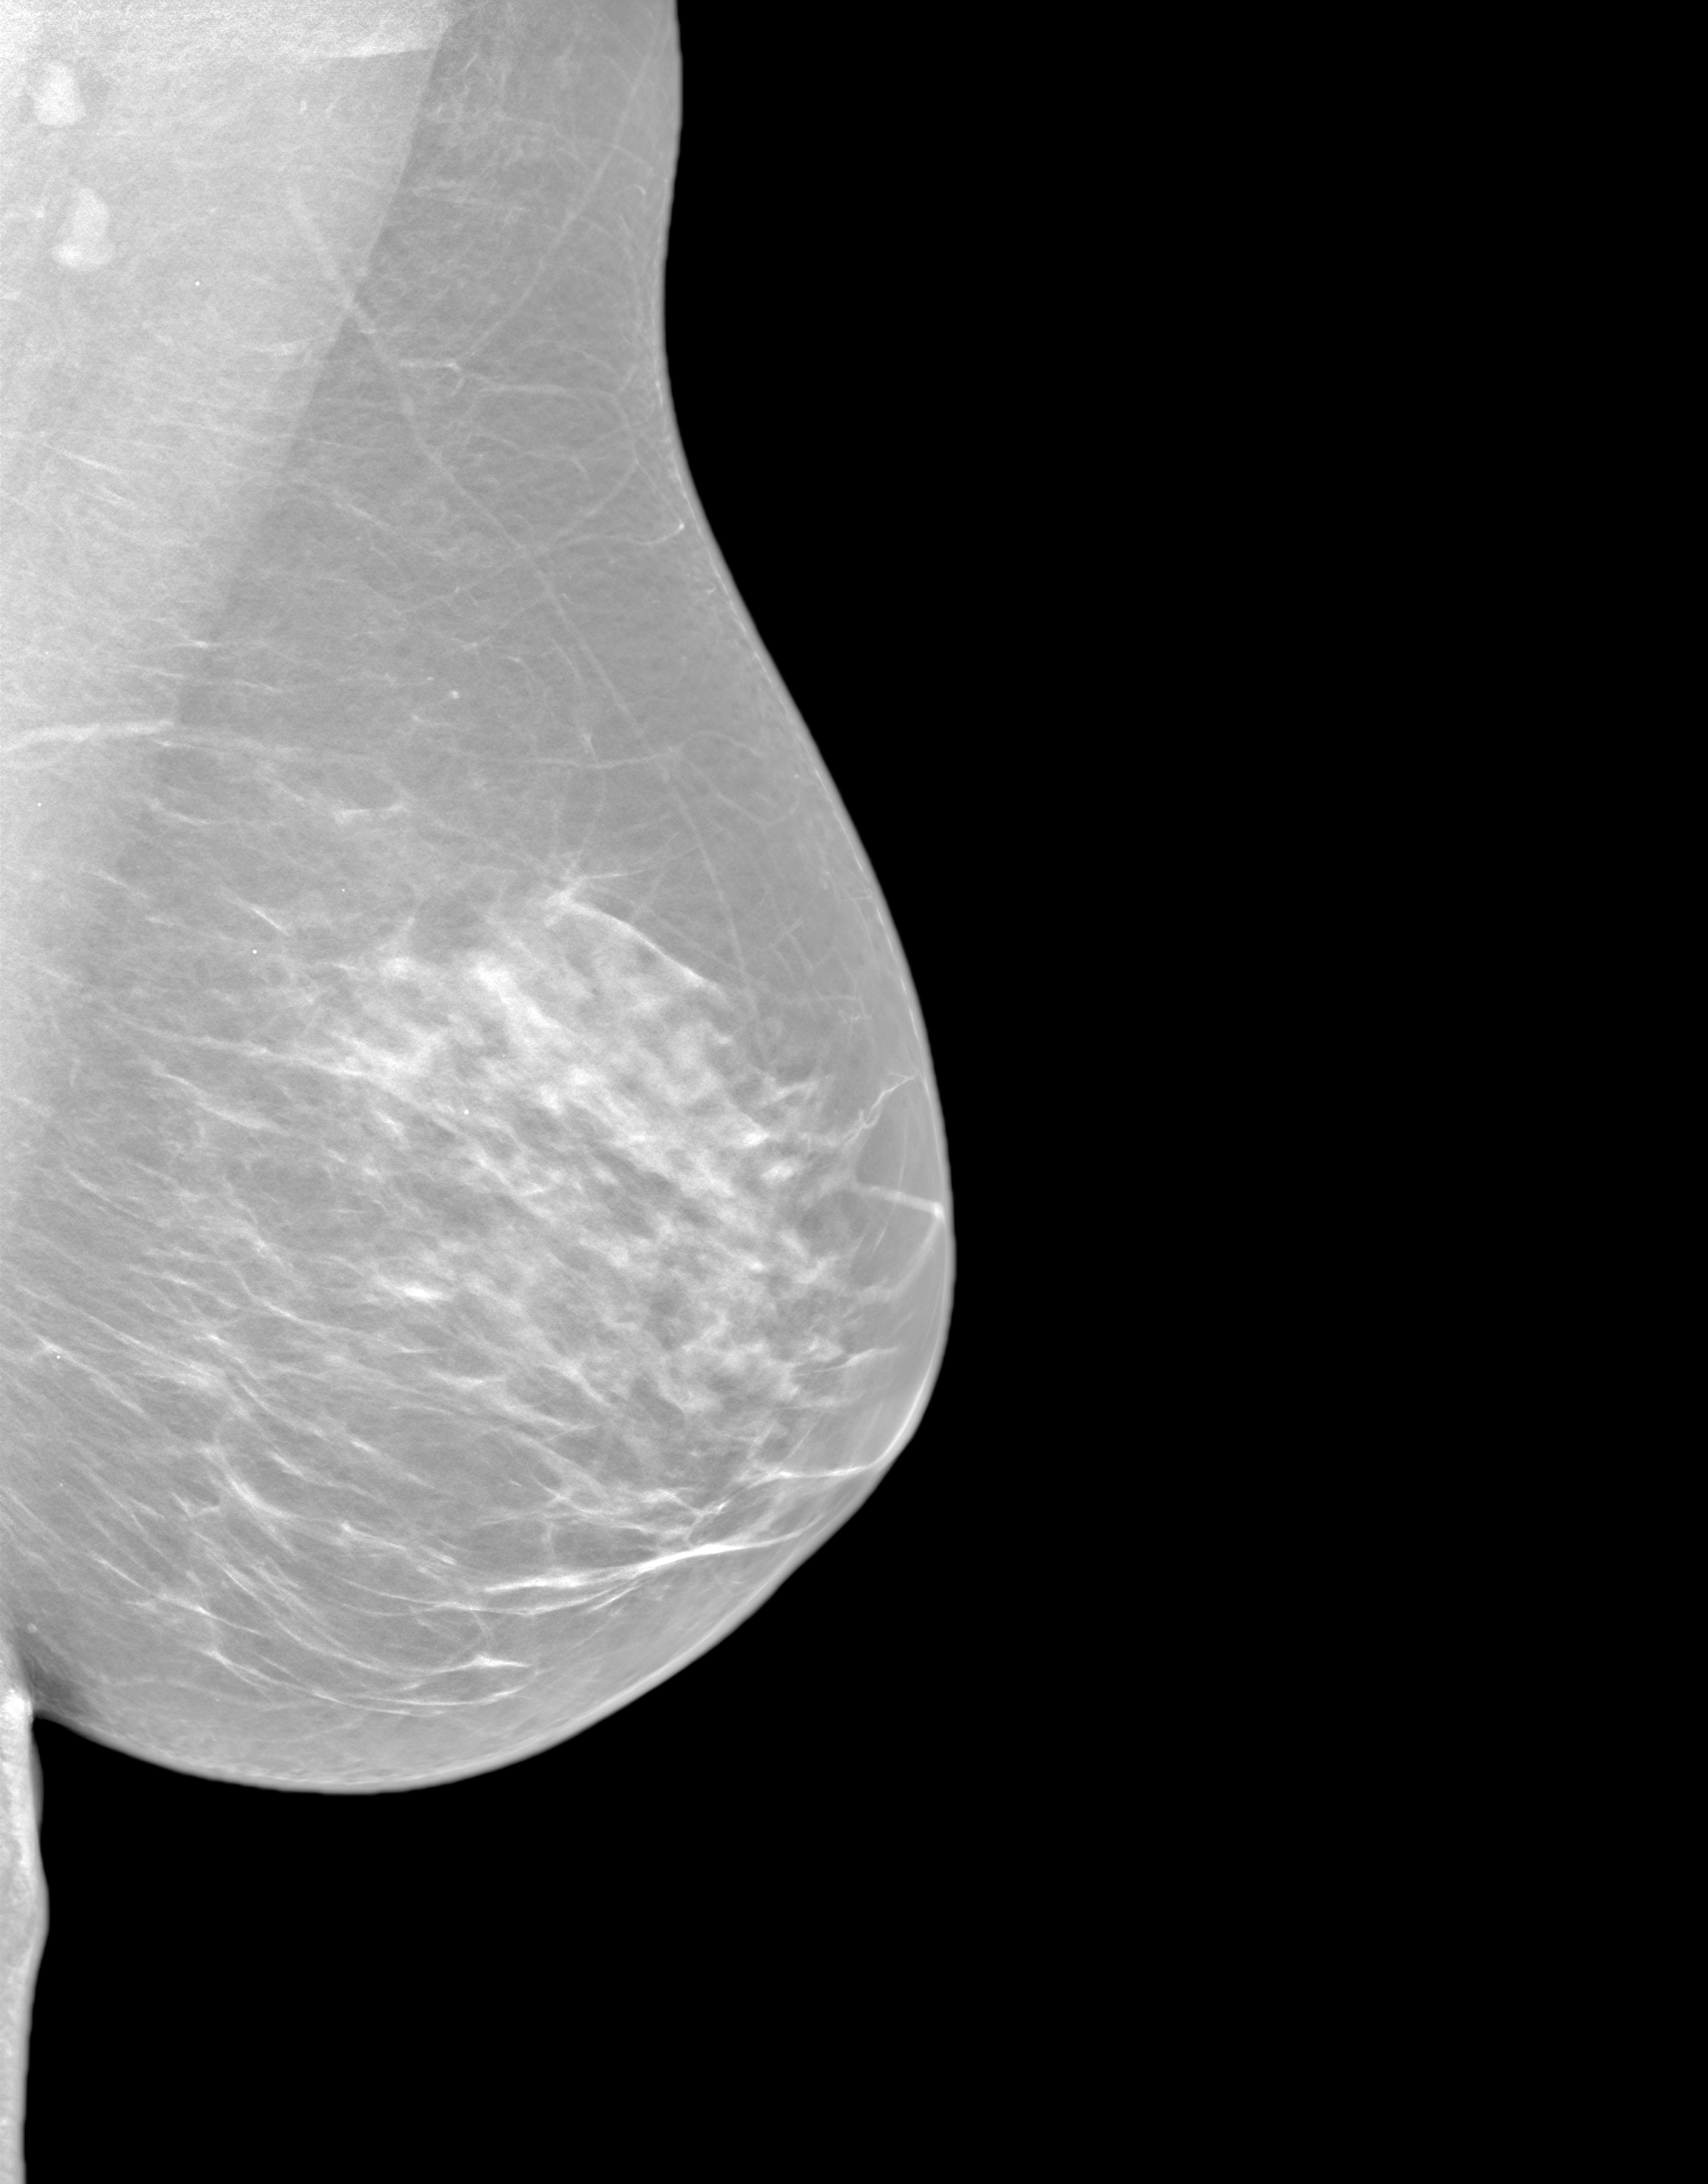
Synthetic 2-D view generated from a tomosynthesis acquisition (not an FFDM exposure), left breast, mediolateral oblique (MLO) view, screening examination. Female patient, age 57 years.
- BI-RADS breast density category at the screening exam (both breasts, scale 1–4): 2
- final BI-RADS assessment for this screening round (tomosynthesis exam, both breasts): category 1
- recall: no recall after this screen